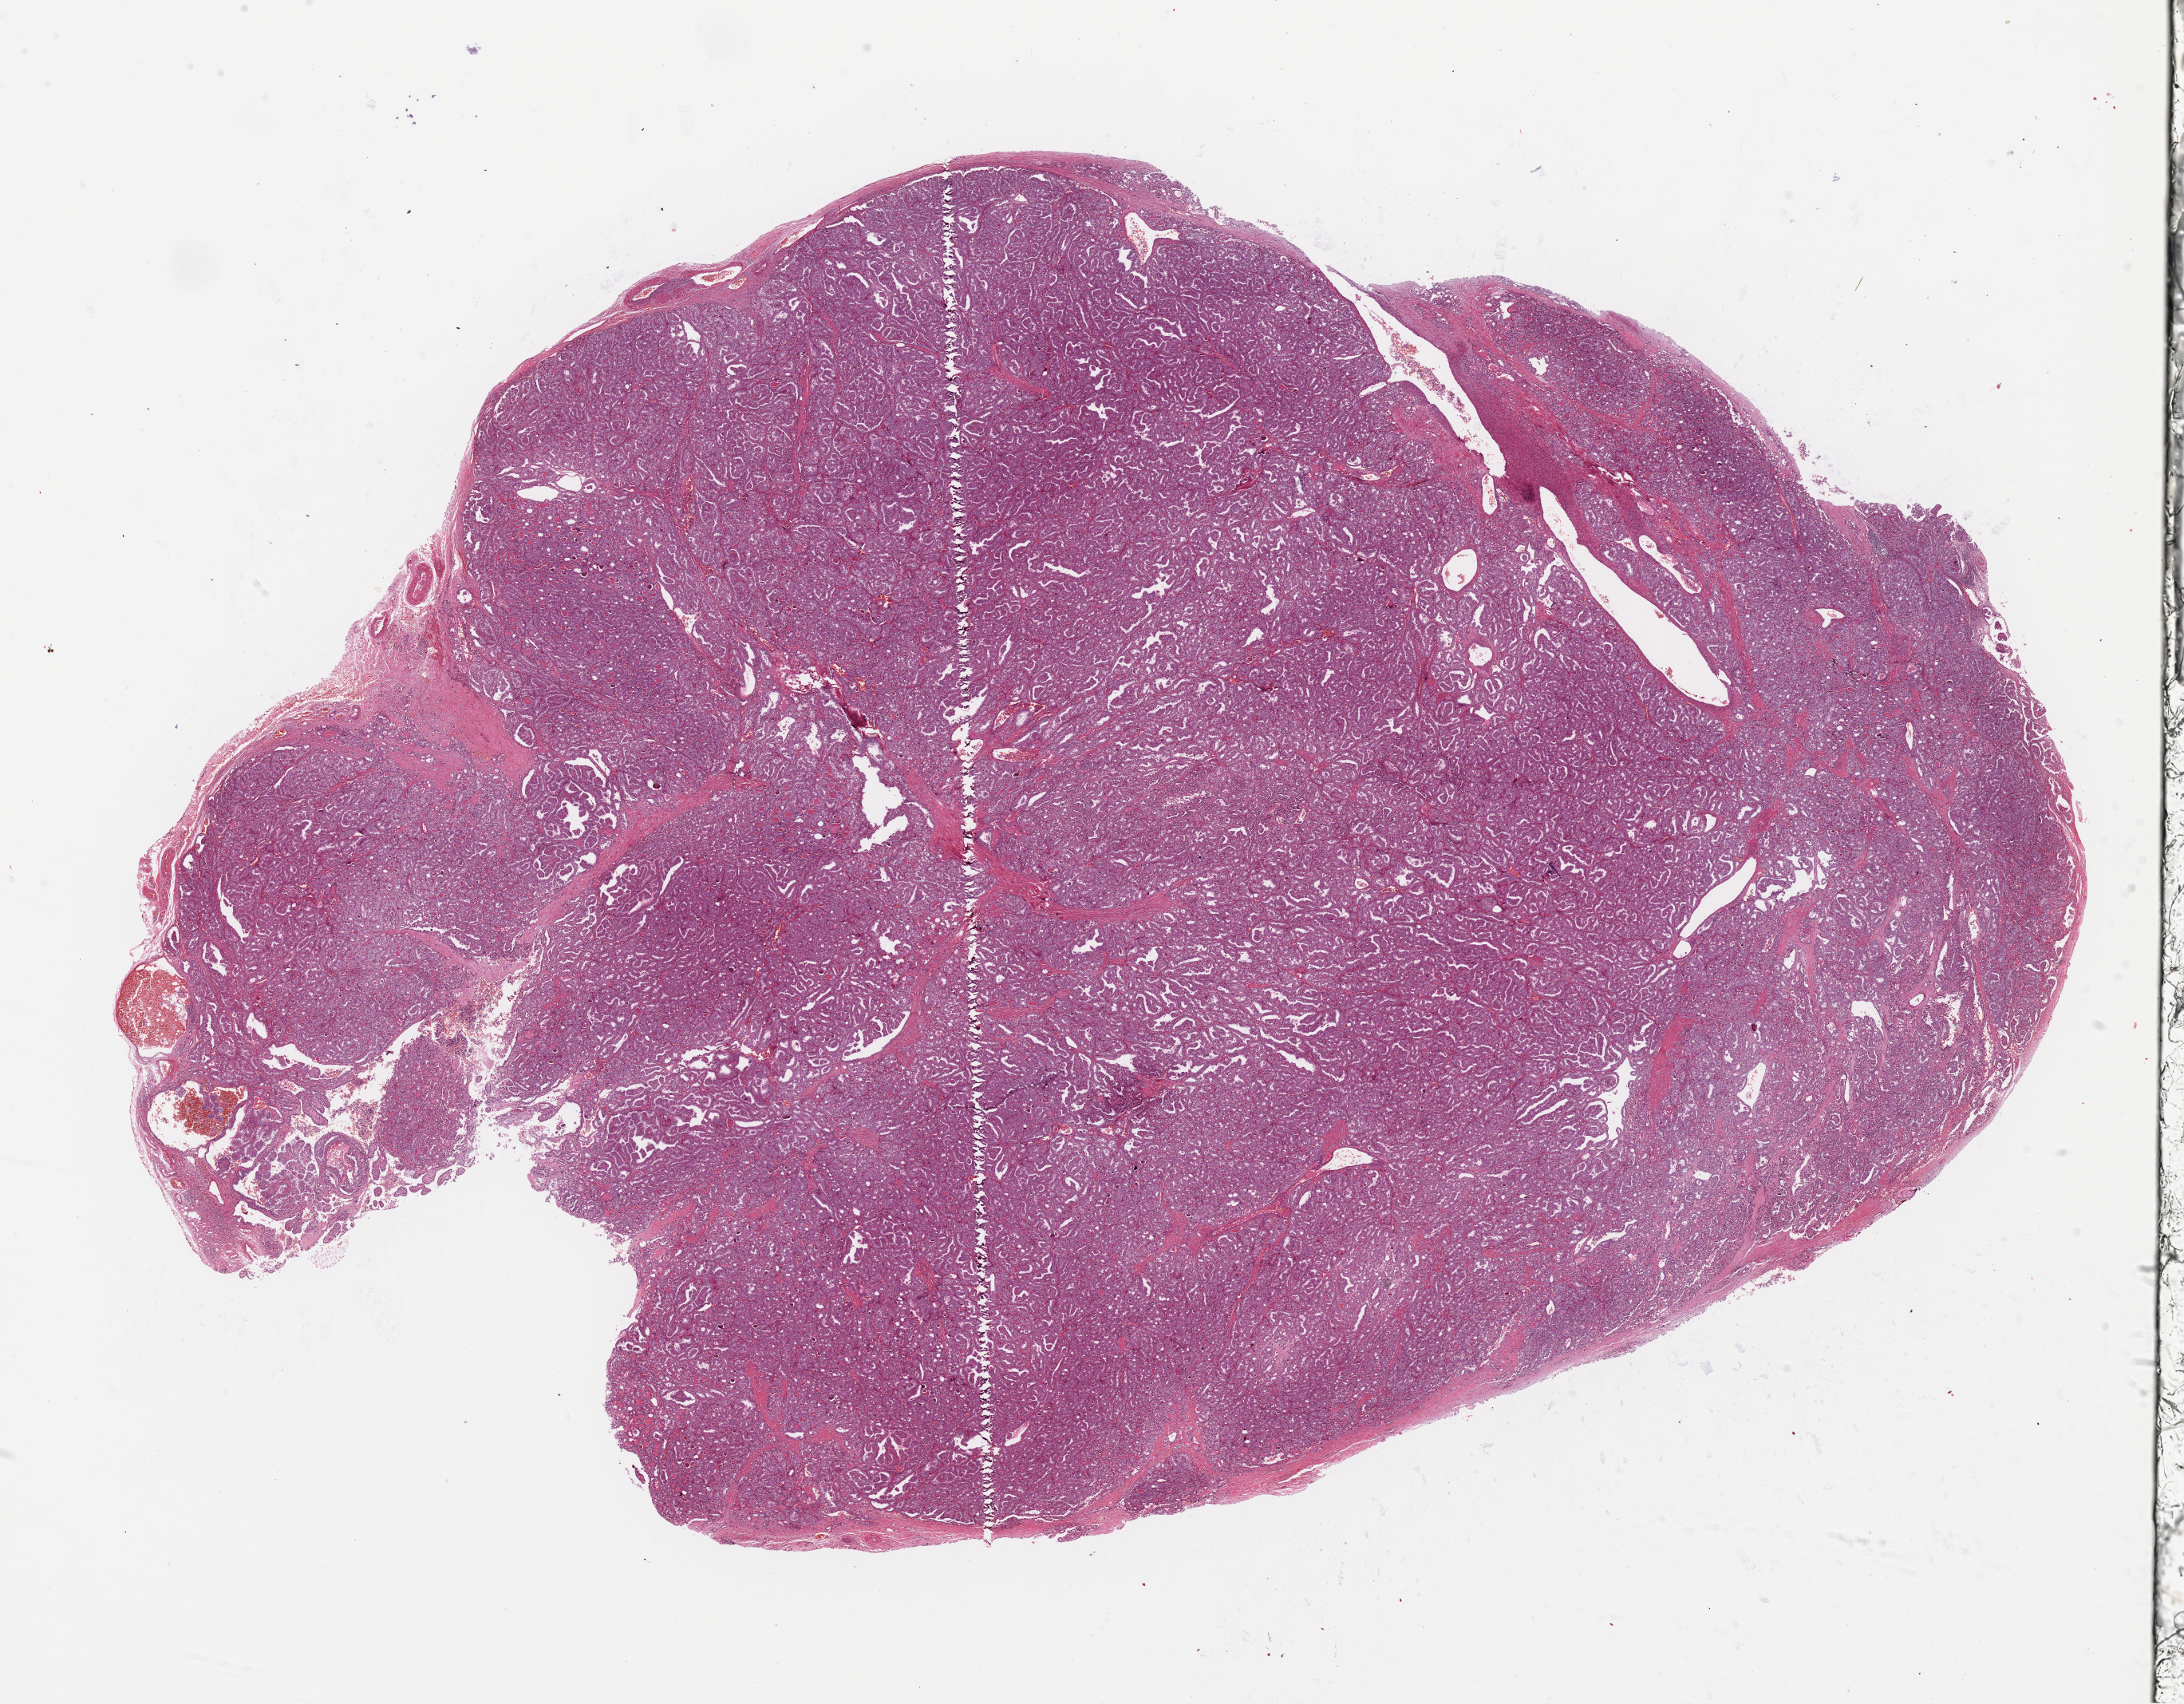
Digitized H&E-stained tissue section (whole slide) — whole scanned area (about 21.6 x 16.9 mm, acquisition: 40x scan) shown as a low-resolution overview, formalin-fixed paraffin-embedded (FFPE) diagnostic section, sample: primary tumour, thyroid. Male, age 31 years at initial diagnosis.
• diagnosis: Papillary adenocarcinoma, NOS (thyroid gland)
• AJCC pathologic stage: I (7th edition)